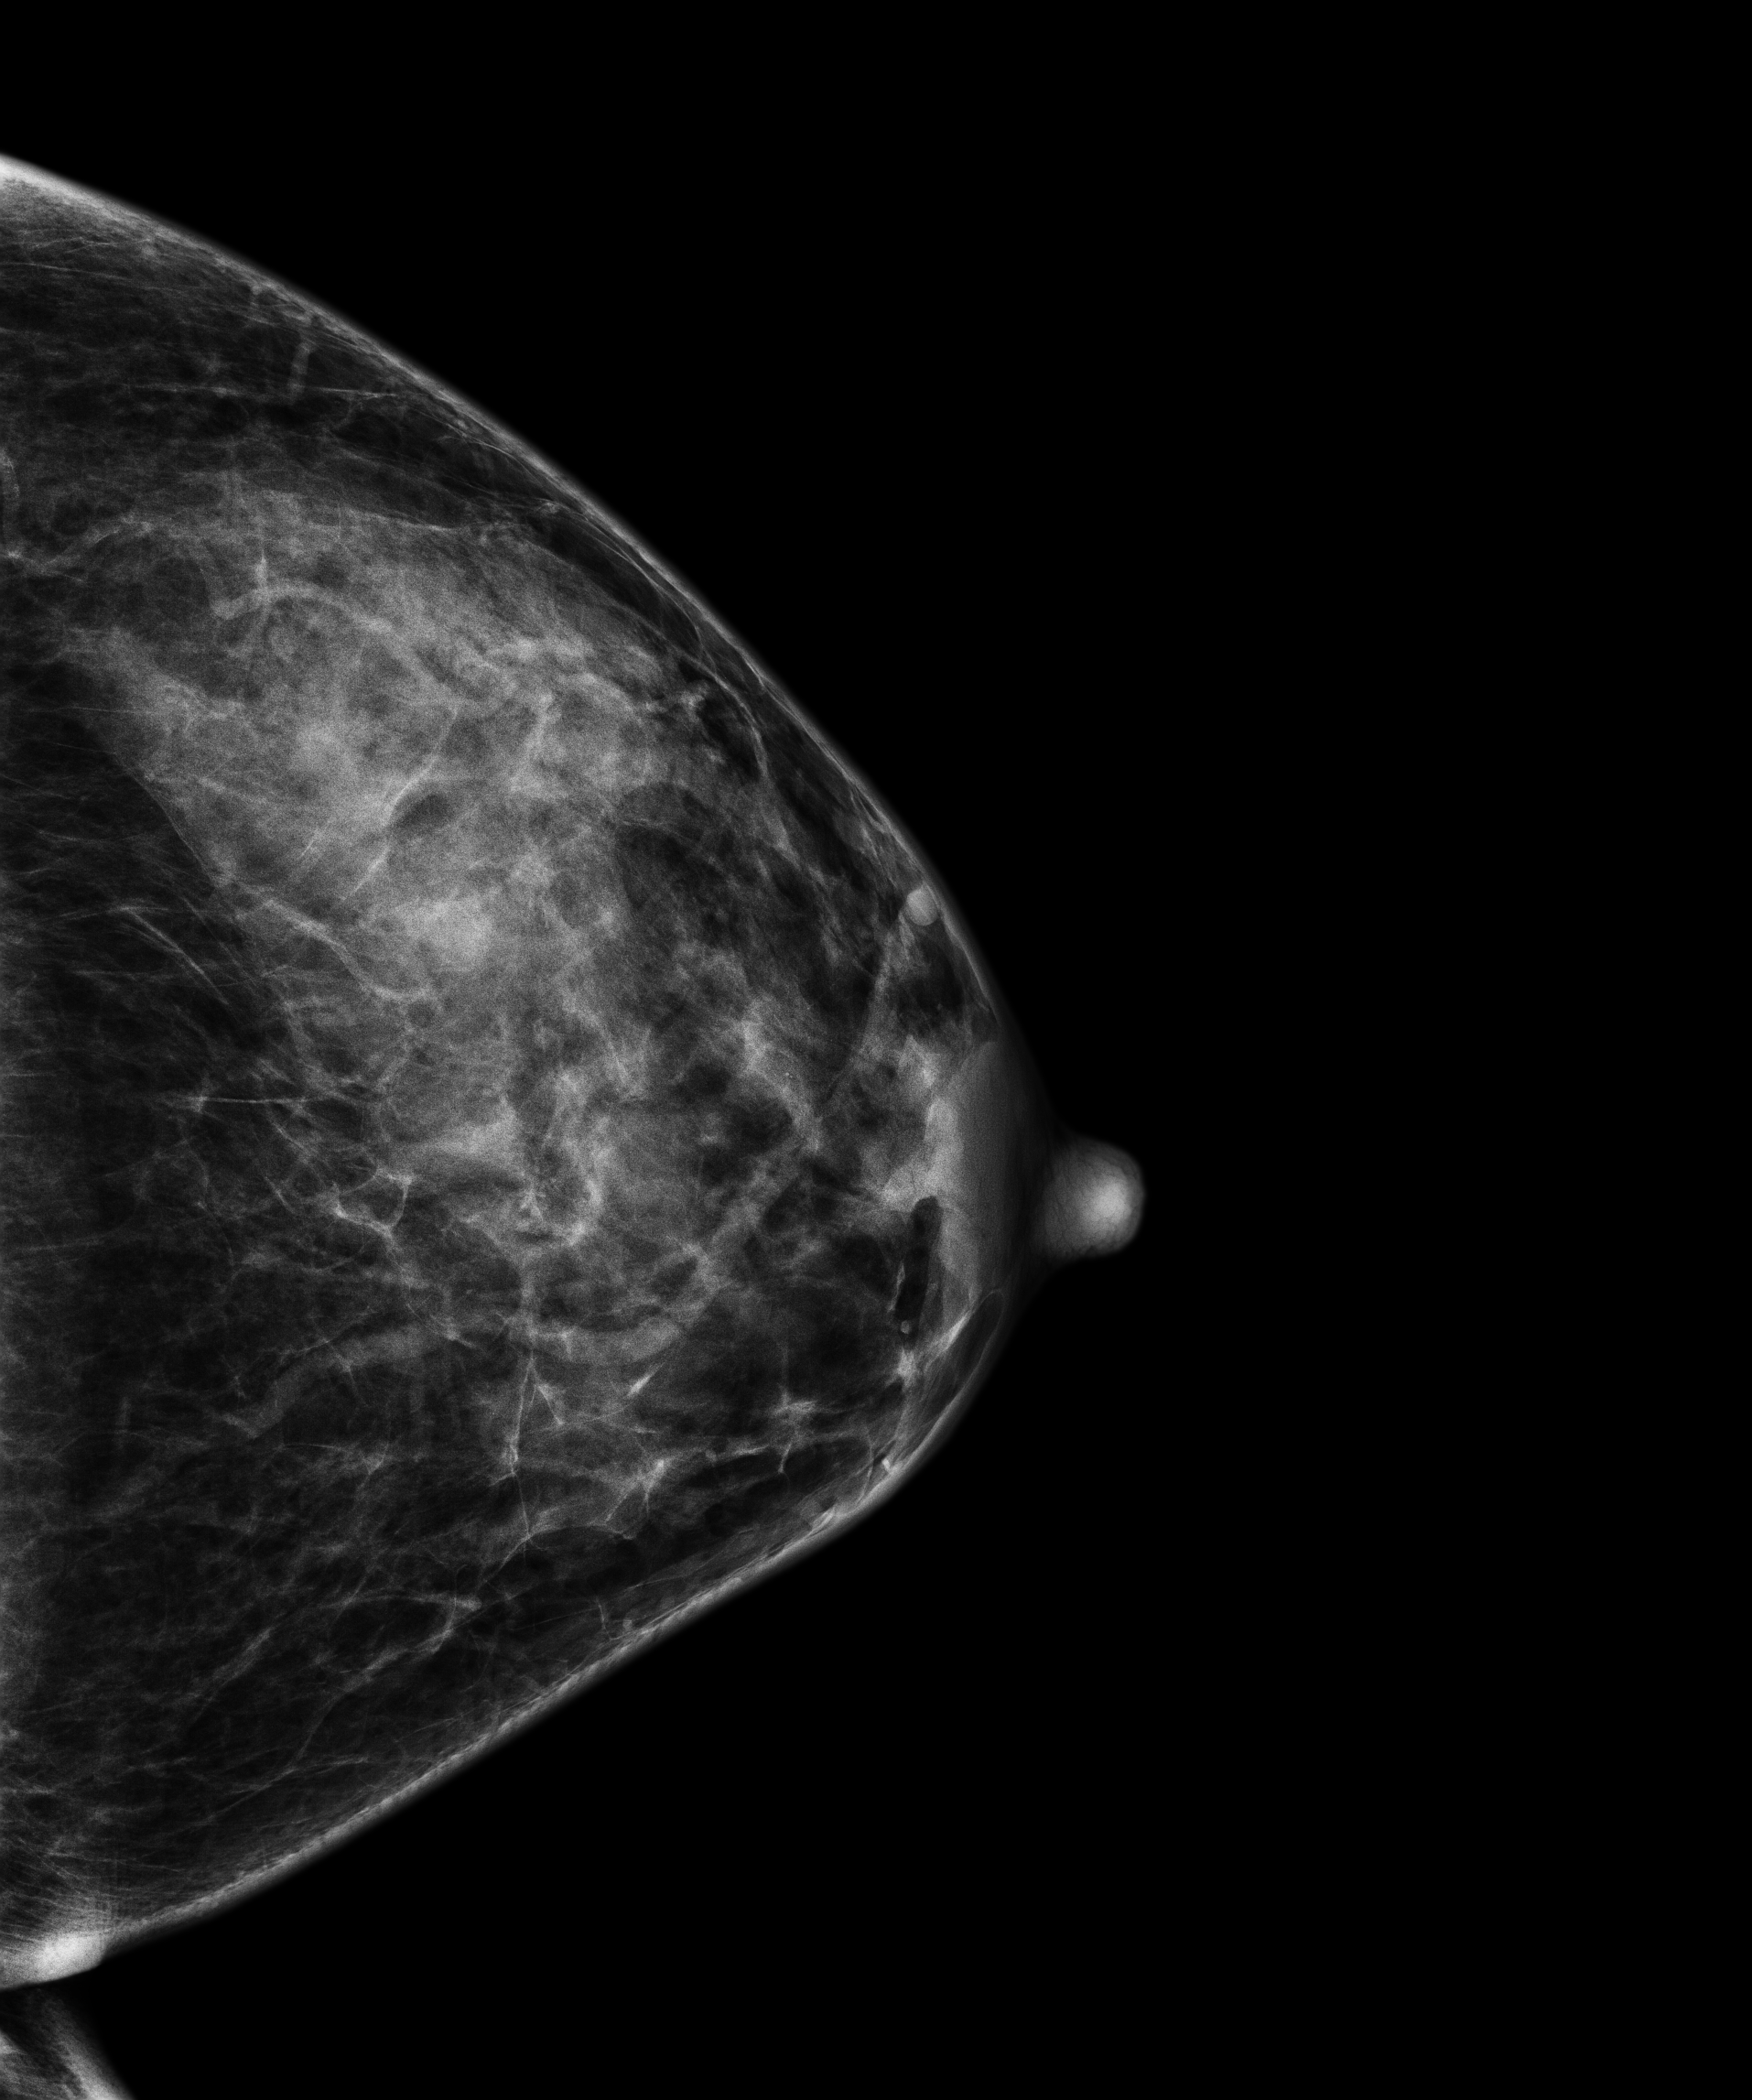
Annual screening mammography examination. Patient: female, 56 years.
Image type: full-field digital mammogram. Breast: left. Projection: cranio-caudal projection.